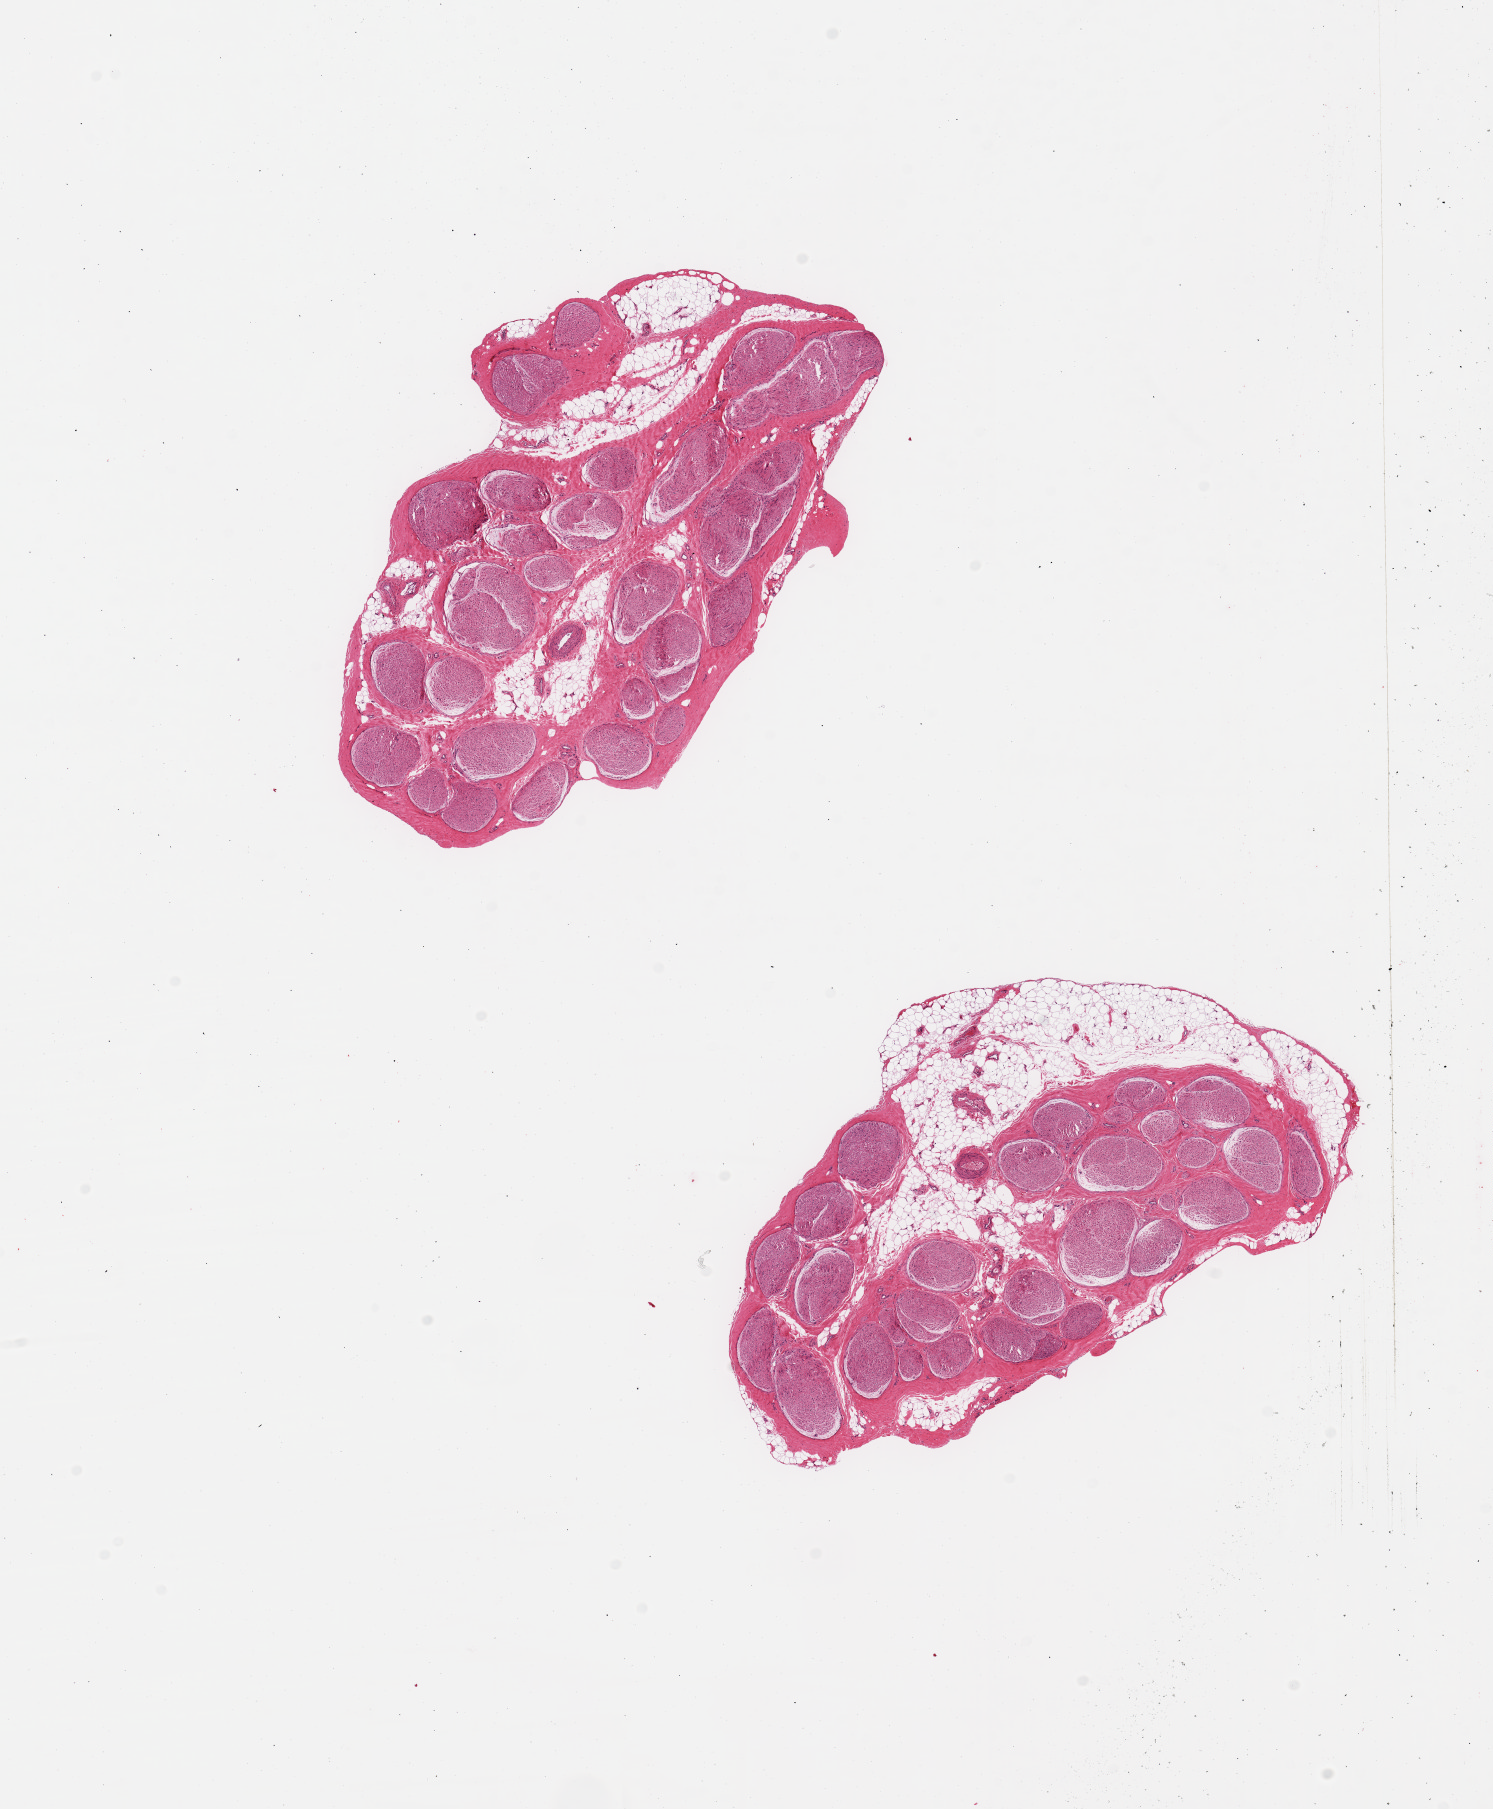
Digitized hematoxylin and eosin (H&E)-stained section — low-resolution overview of the scanned area, about 11.8 x 14.3 mm; PAXgene-fixed, paraffin-embedded tissue; section of tibial nerve (target tissue); donor tissue sample. Donor sex: female.
• reviewer comment on this tissue sample: 2 pieces; 30% fat content